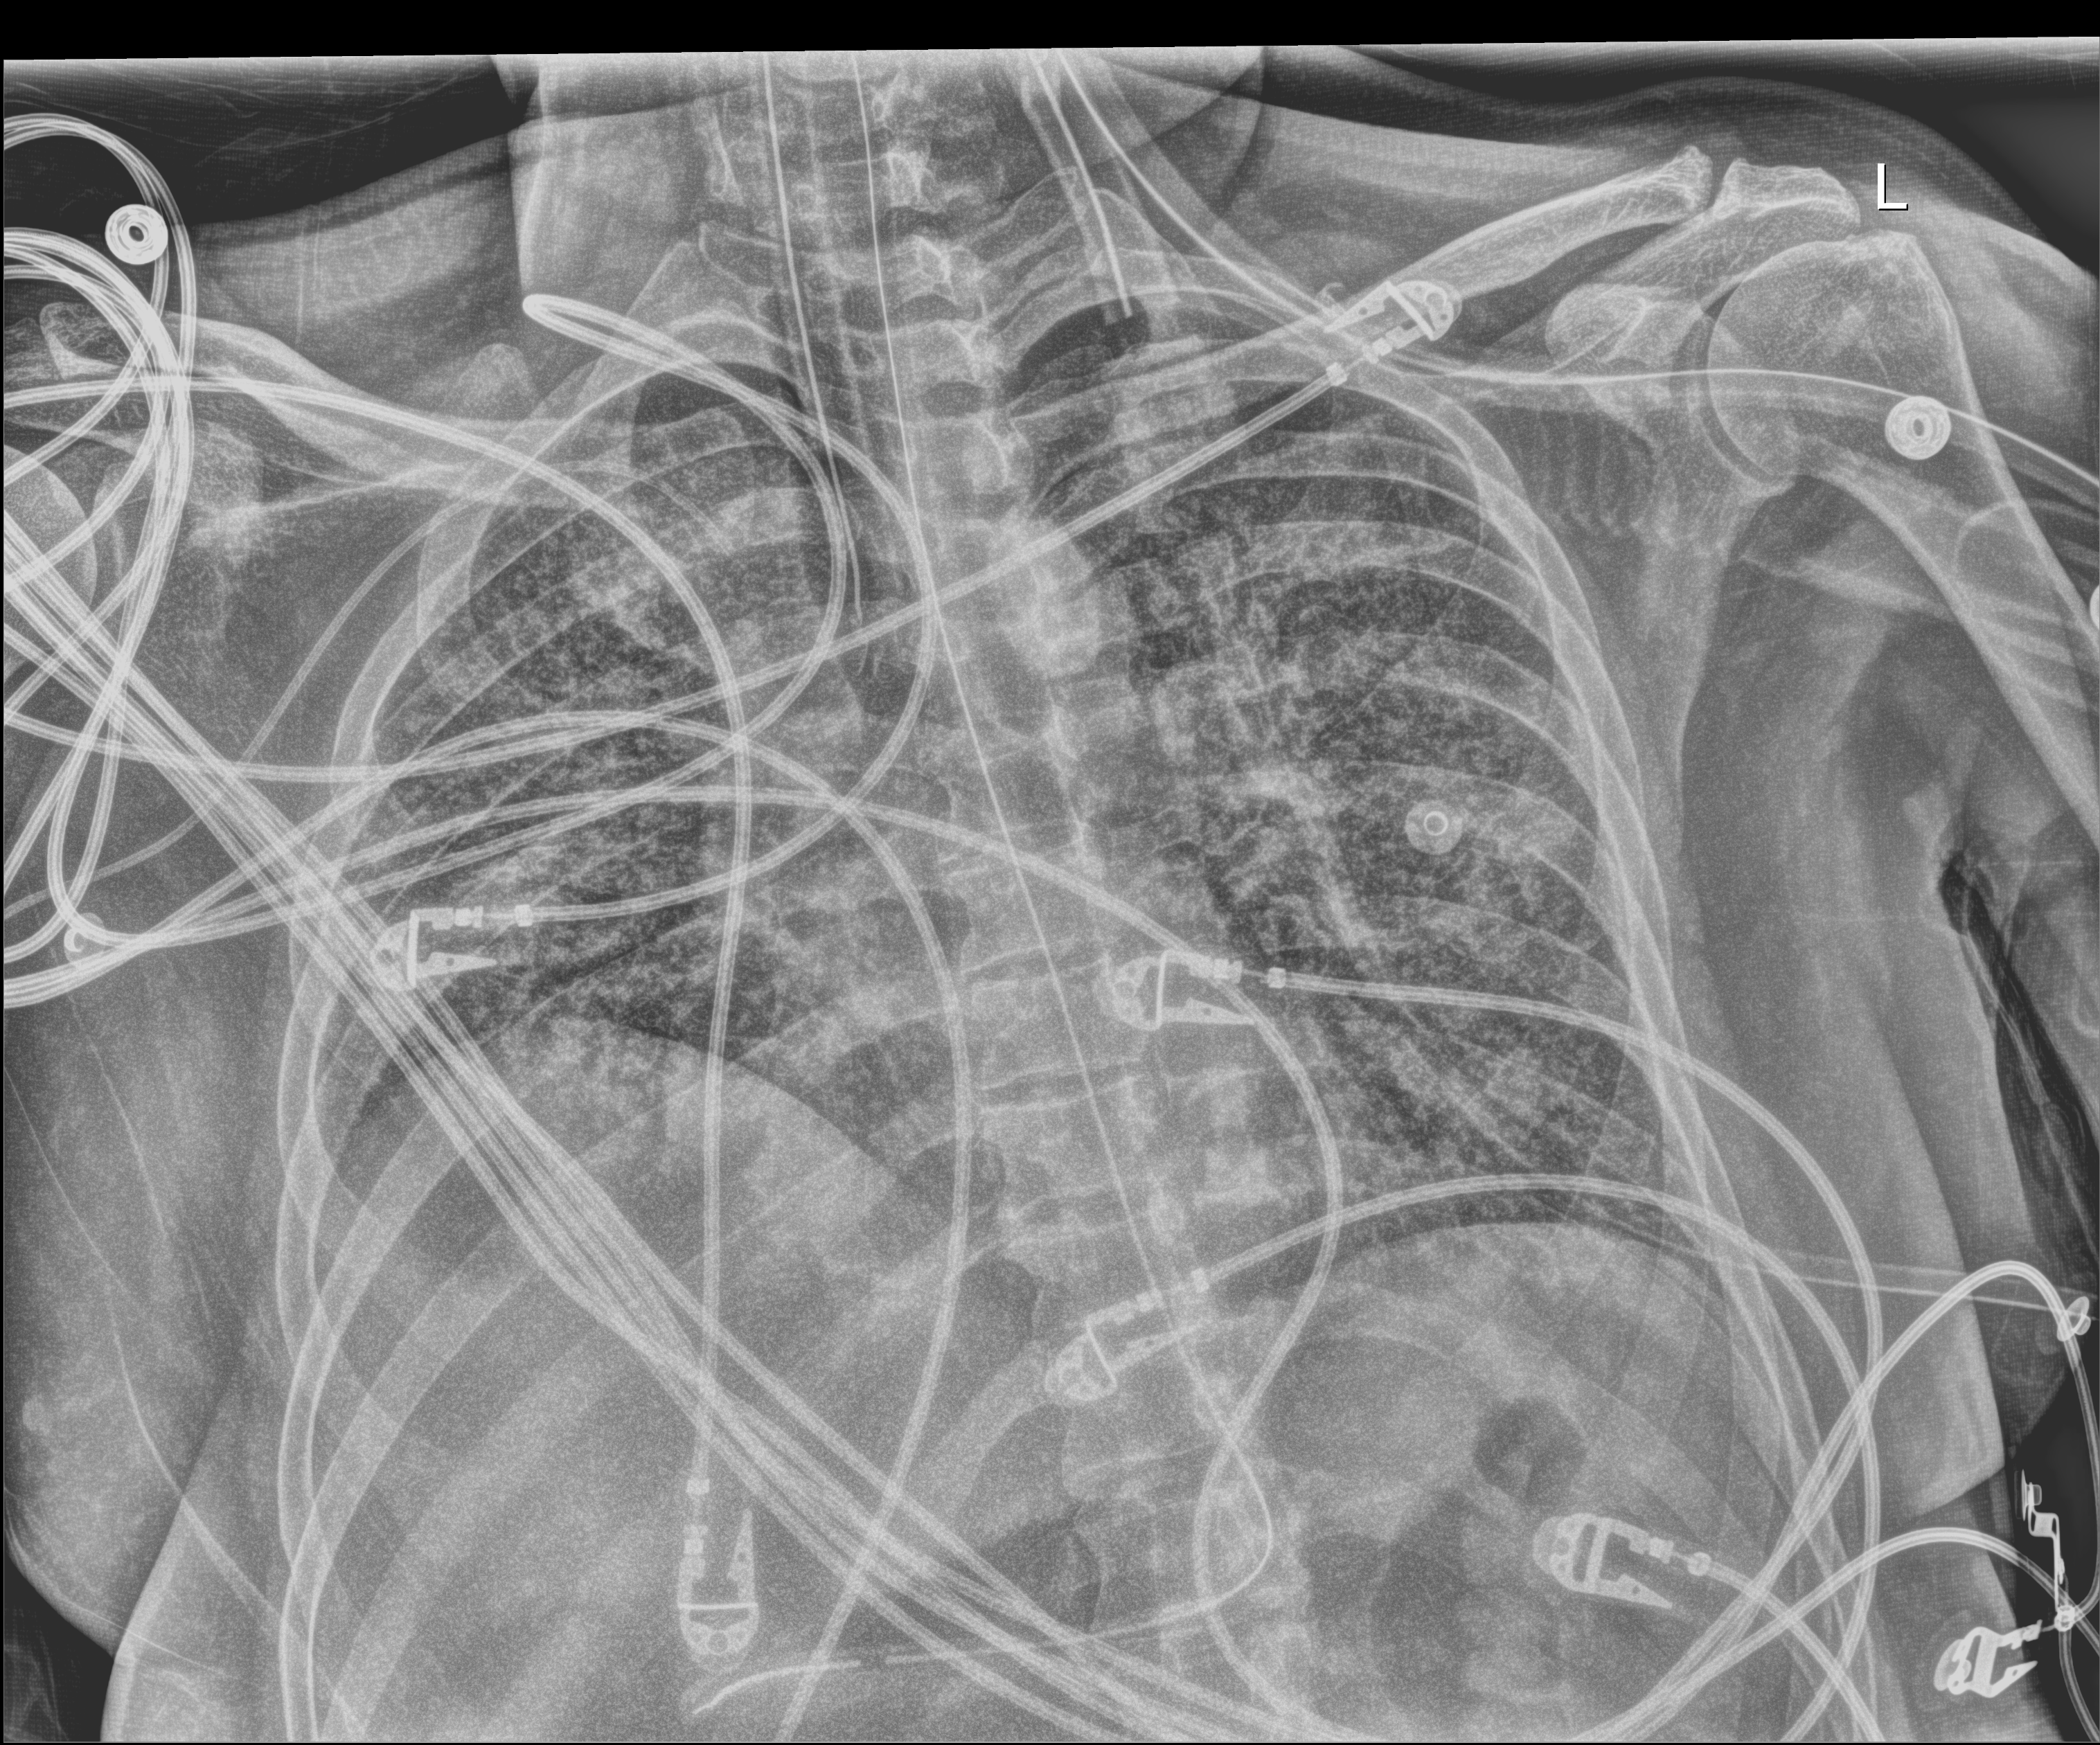
Portable chest radiograph, anteroposterior (AP) projection. Patient hospitalised with COVID-19; male, aged 18–59 years.
From the hospital-stay record, not from the radiograph (when in the stay this image was taken is not recorded):
- diabetes (admission record): no